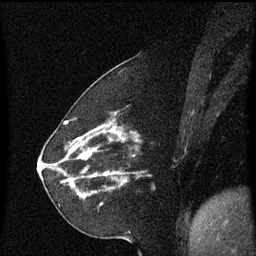
Breast MRI (dynamic contrast-enhanced), one sagittal slice. Slice 20 of 60 in the series (ordered by position). Dynamic contrast-enhanced series, image 2 of 3 at this slice position (ordered by acquisition). 1.5 T. TE 4.2 ms, TR 8.4 ms. 2.2 mm slice thickness. 256 × 256 image matrix, field of view 200 × 200 mm. Patient: female, 60 years. From the clinical record (not read from this slice): setting: breast cancer imaged before/during neoadjuvant chemotherapy; receptor status: triple-negative.
Structures marked on this image (semi-automatic segmentation, software-assisted and operator-edited):
- analysis volume of interest (the breast-tissue region the enhancement analysis was run in; not a lesion): box from (x=68, y=142) to (x=139, y=209) px
- tumour enhancement mask (voxels above the 70 % enhancement threshold inside the analysis volume of interest): (x=70, y=148)–(x=96, y=193)